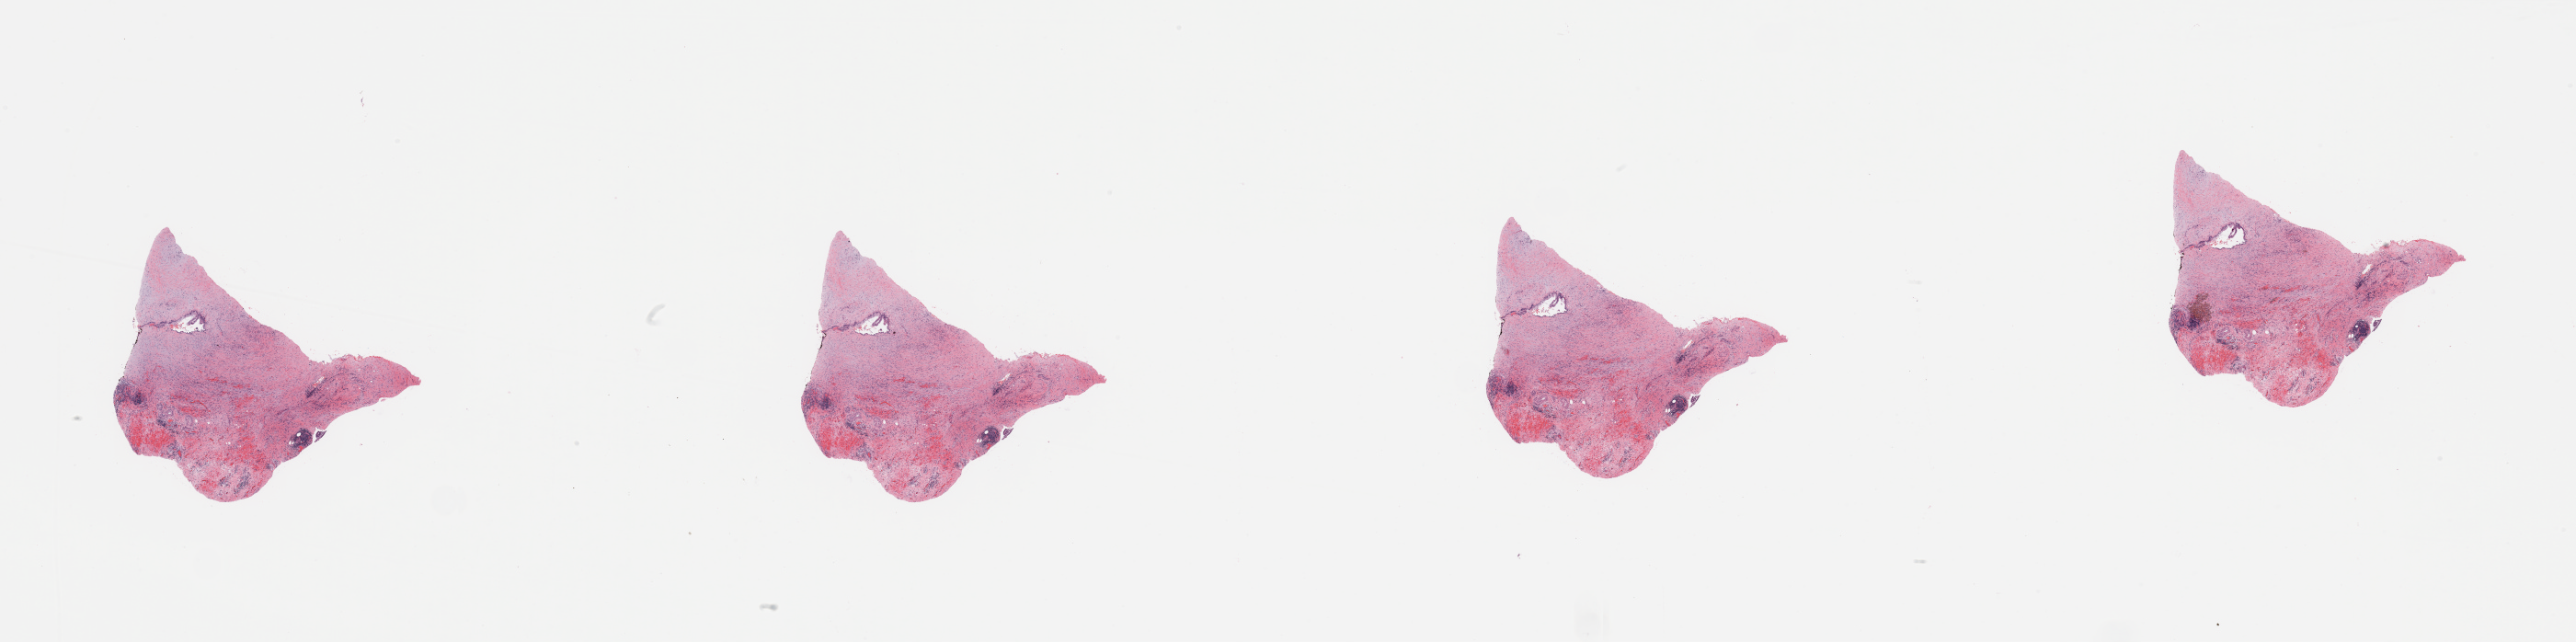
Digitized H&E tissue section (whole slide) — low-resolution overview of the scanned area, about 44.3 x 11.0 mm; tumour tissue sample, pancreas. 62-year-old male patient. Histologic grade: G3 (poorly differentiated).
Histologic diagnosis: Infiltrating duct carcinoma, NOS. AJCC pathologic stage: IIA.